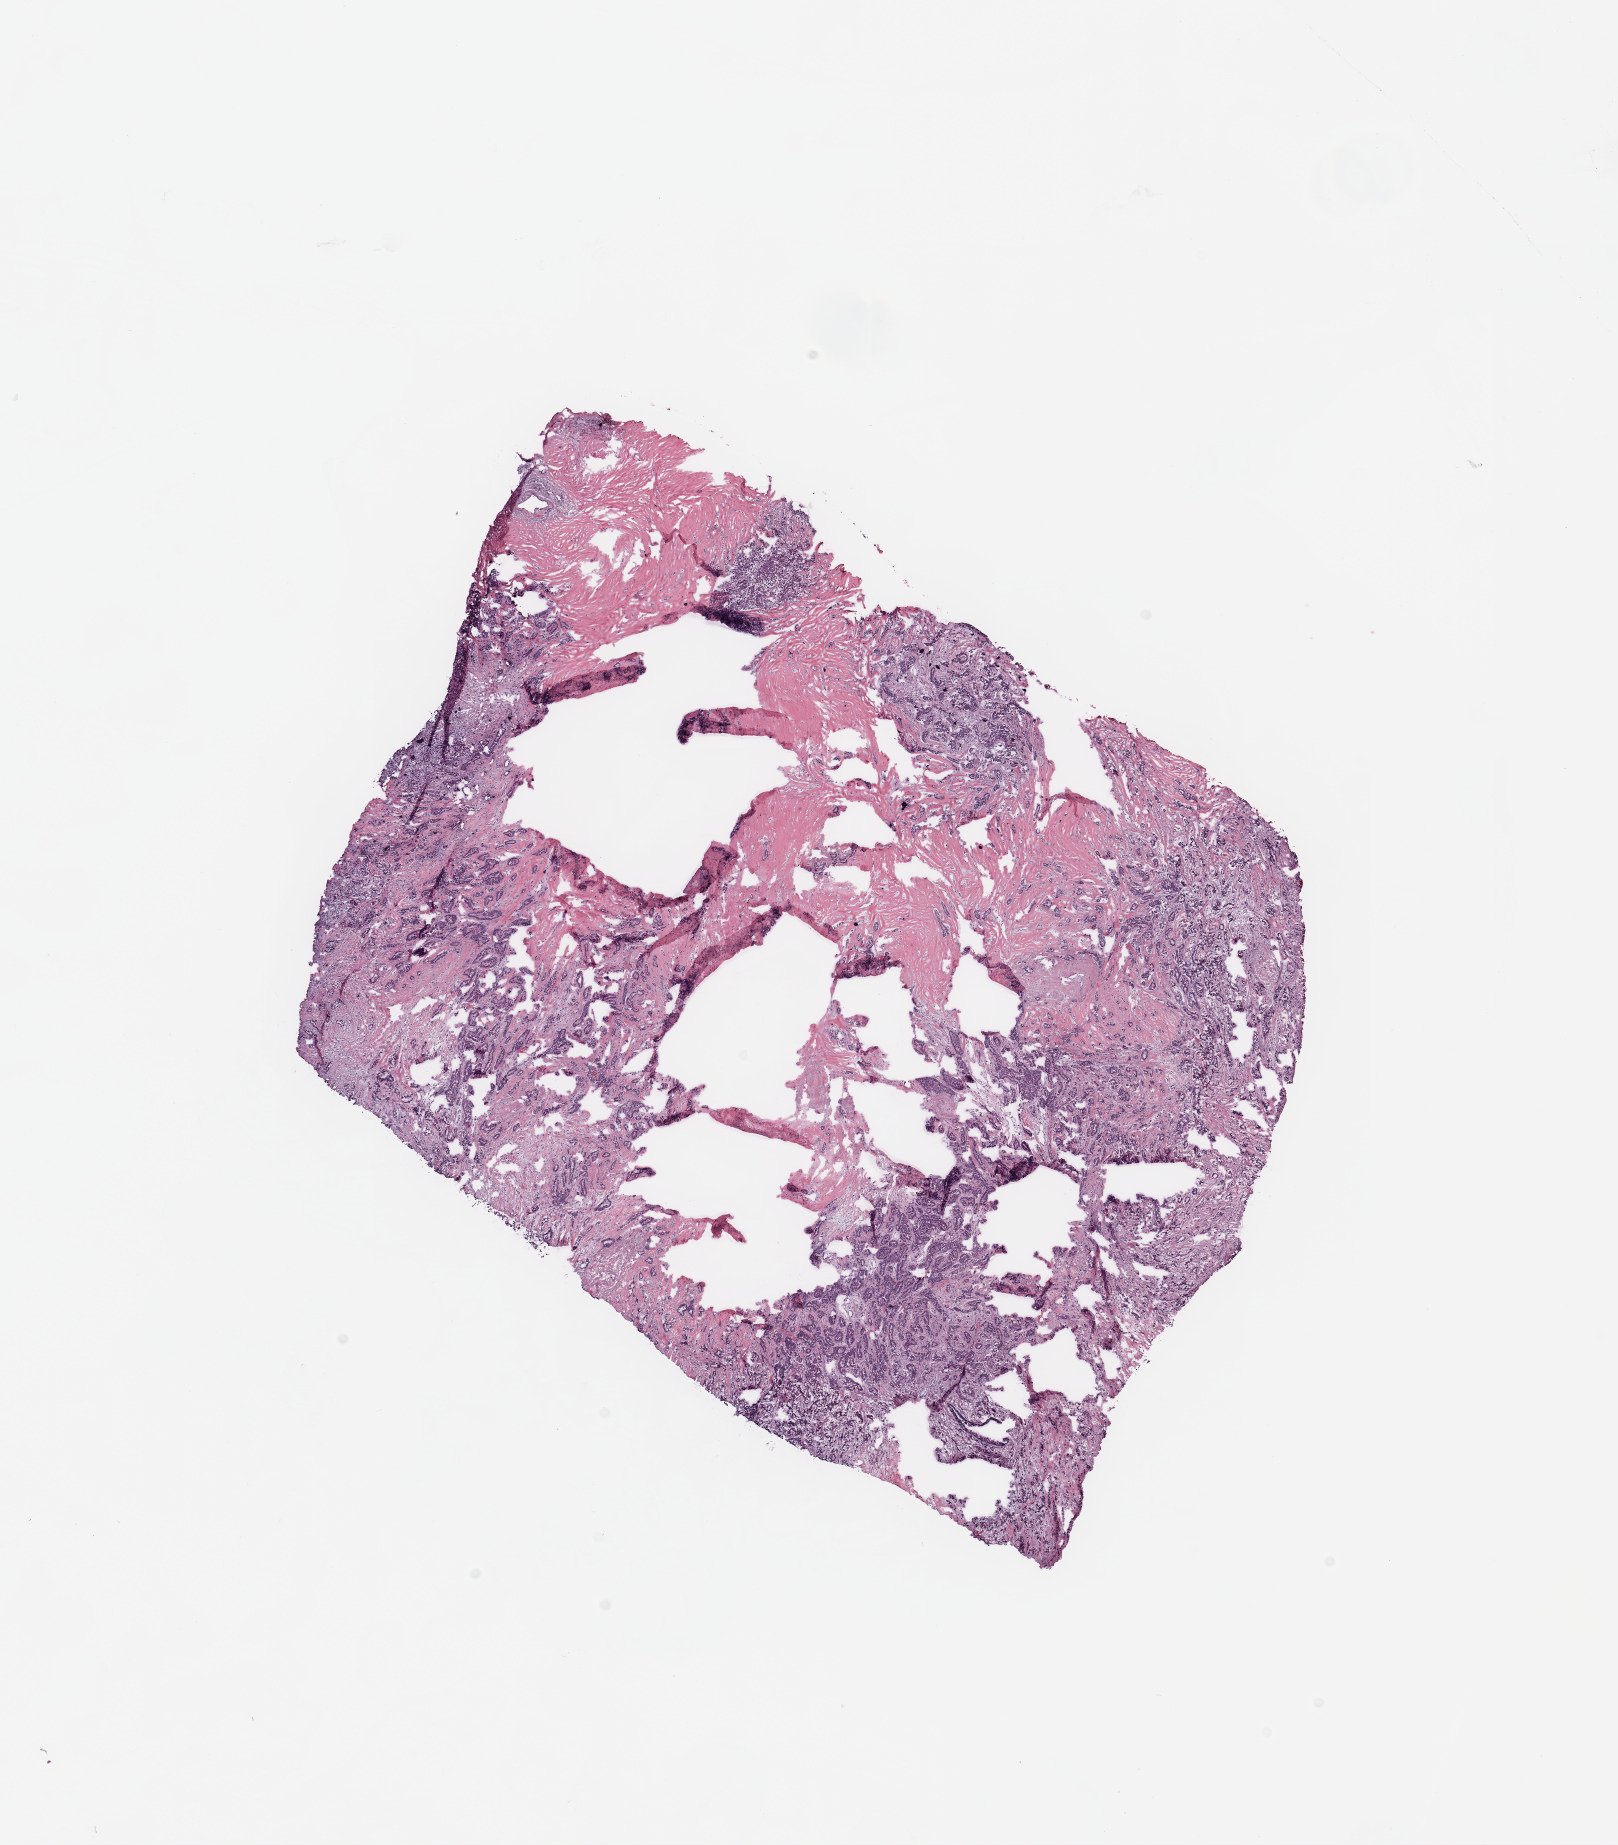
Whole-slide histology image, H&E, whole scanned area (about 12.8 x 14.6 mm, from a 20x scan) shown as a low-resolution overview; breast, tumour tissue. Female, 50 y/o.
* diagnosis: Infiltrating duct carcinoma, NOS
* AJCC pathologic stage: IA